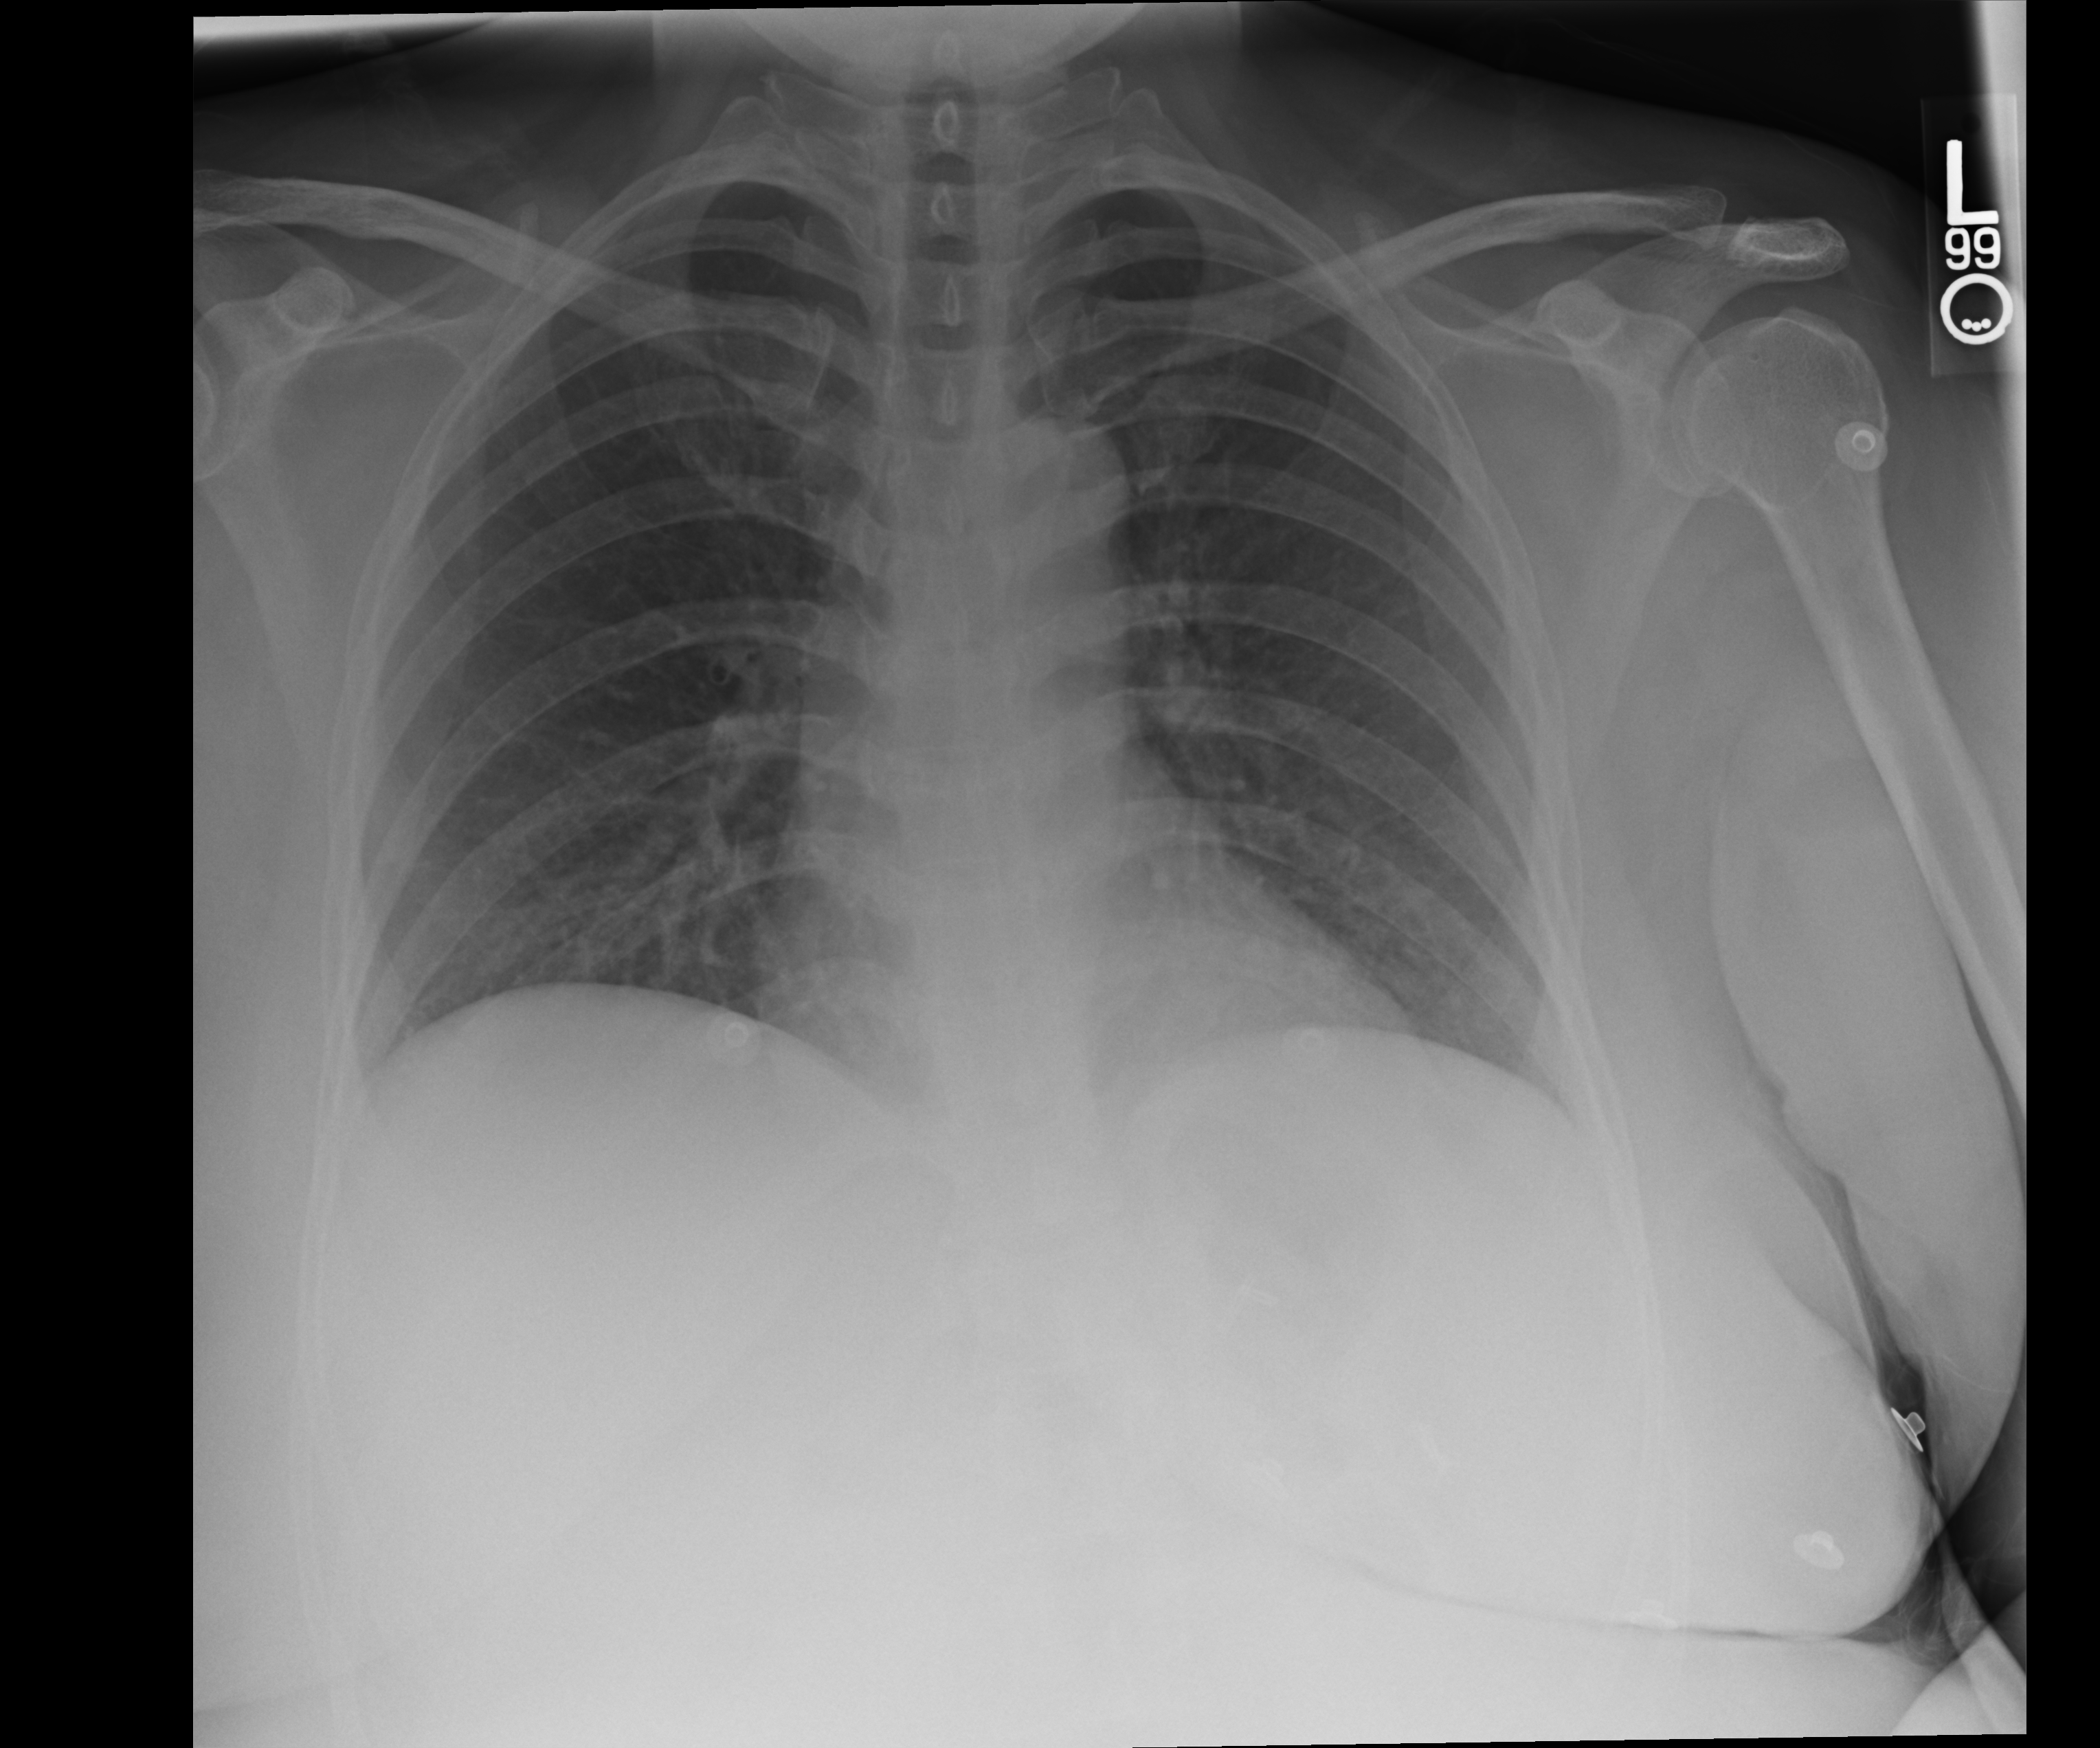
Chest radiograph. Patient hospitalised with COVID-19; female, aged 18–59 years.
Admission-level facts for this patient (not findings on this image; timing relative to this image not recorded):
- length of hospital stay: 5 days
- diabetes (admission record): yes
- smoking status (admission record): former